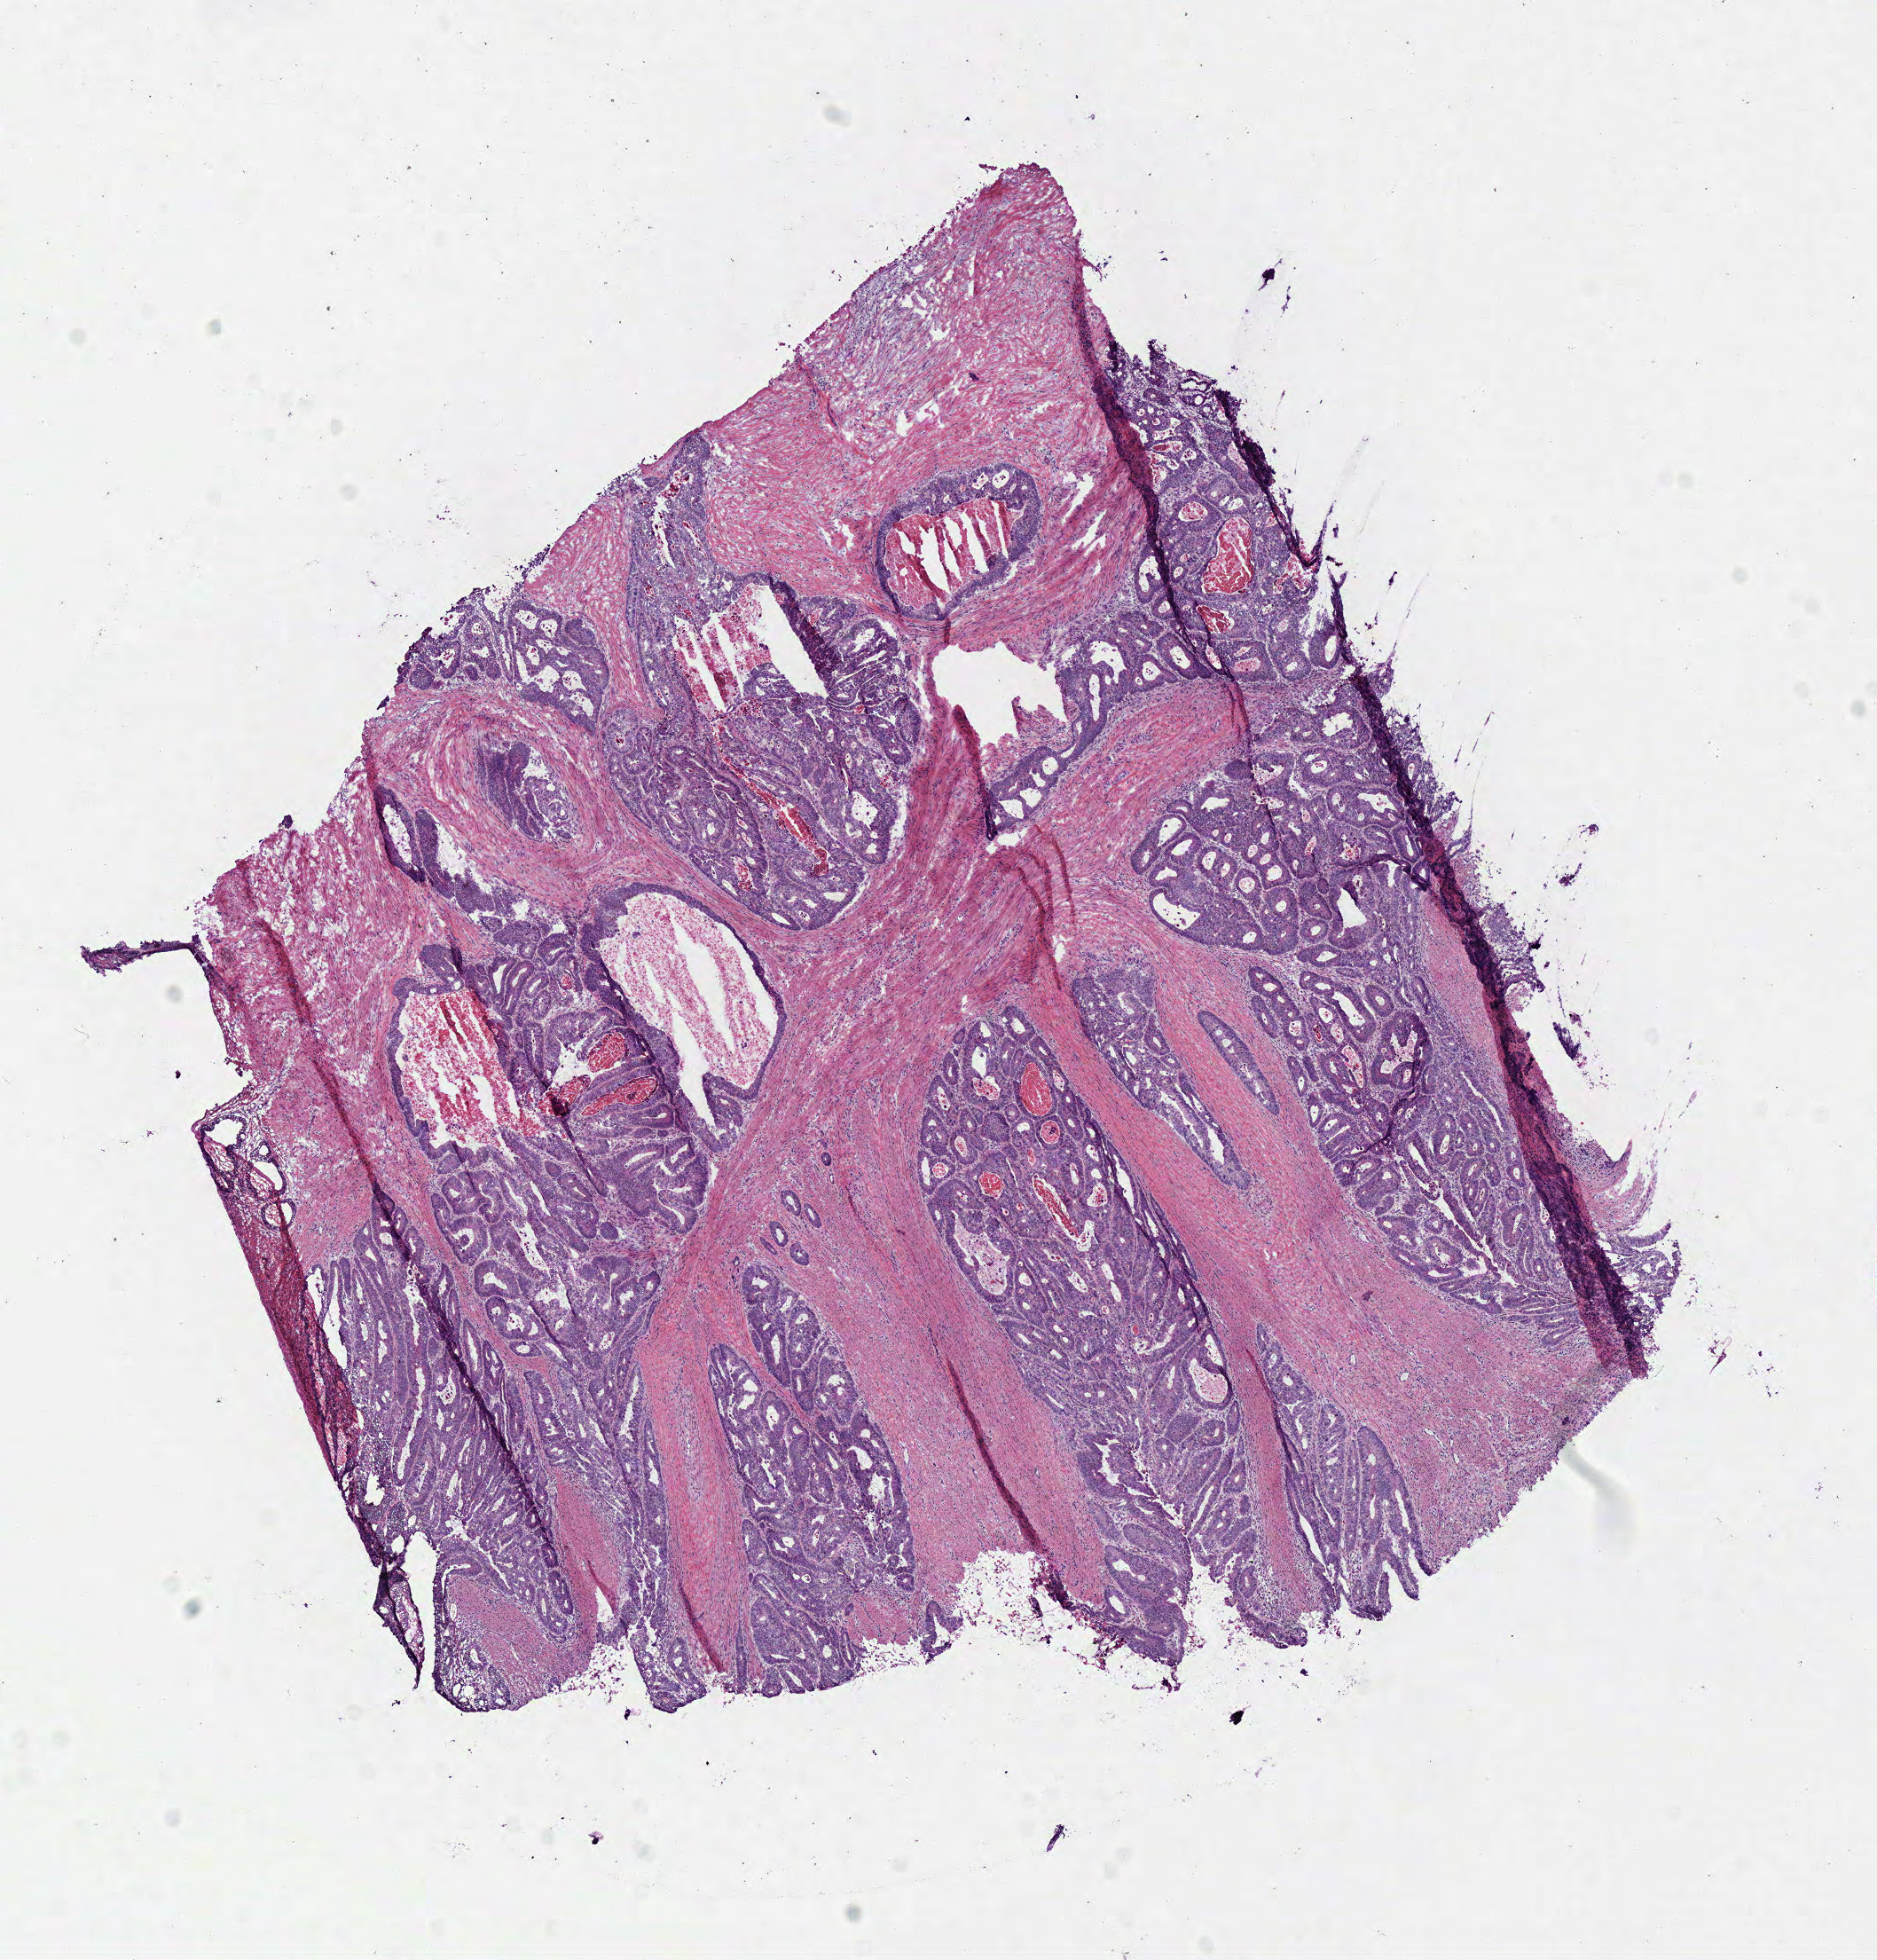
Whole-slide histology image, H&E-stained, shown as a low-resolution overview of the whole scanned area (about 8.3 x 8.7 mm, slide scanned at 40x), frozen section from the bottom of the tissue portion, sample: primary tumour, rectum. Female patient; age at initial diagnosis 59 years. Pathologist review of this section (percent, as recorded): tumour cells 52%, tumour nuclei 80%, normal cells 0%, stromal cells 40%, necrosis 8%.
Histologic diagnosis: Adenocarcinoma in tubulovillous adenoma. AJCC pathologic stage: IIA (7th edition). Lymph nodes positive (case pathology): 0 of 8 examined.